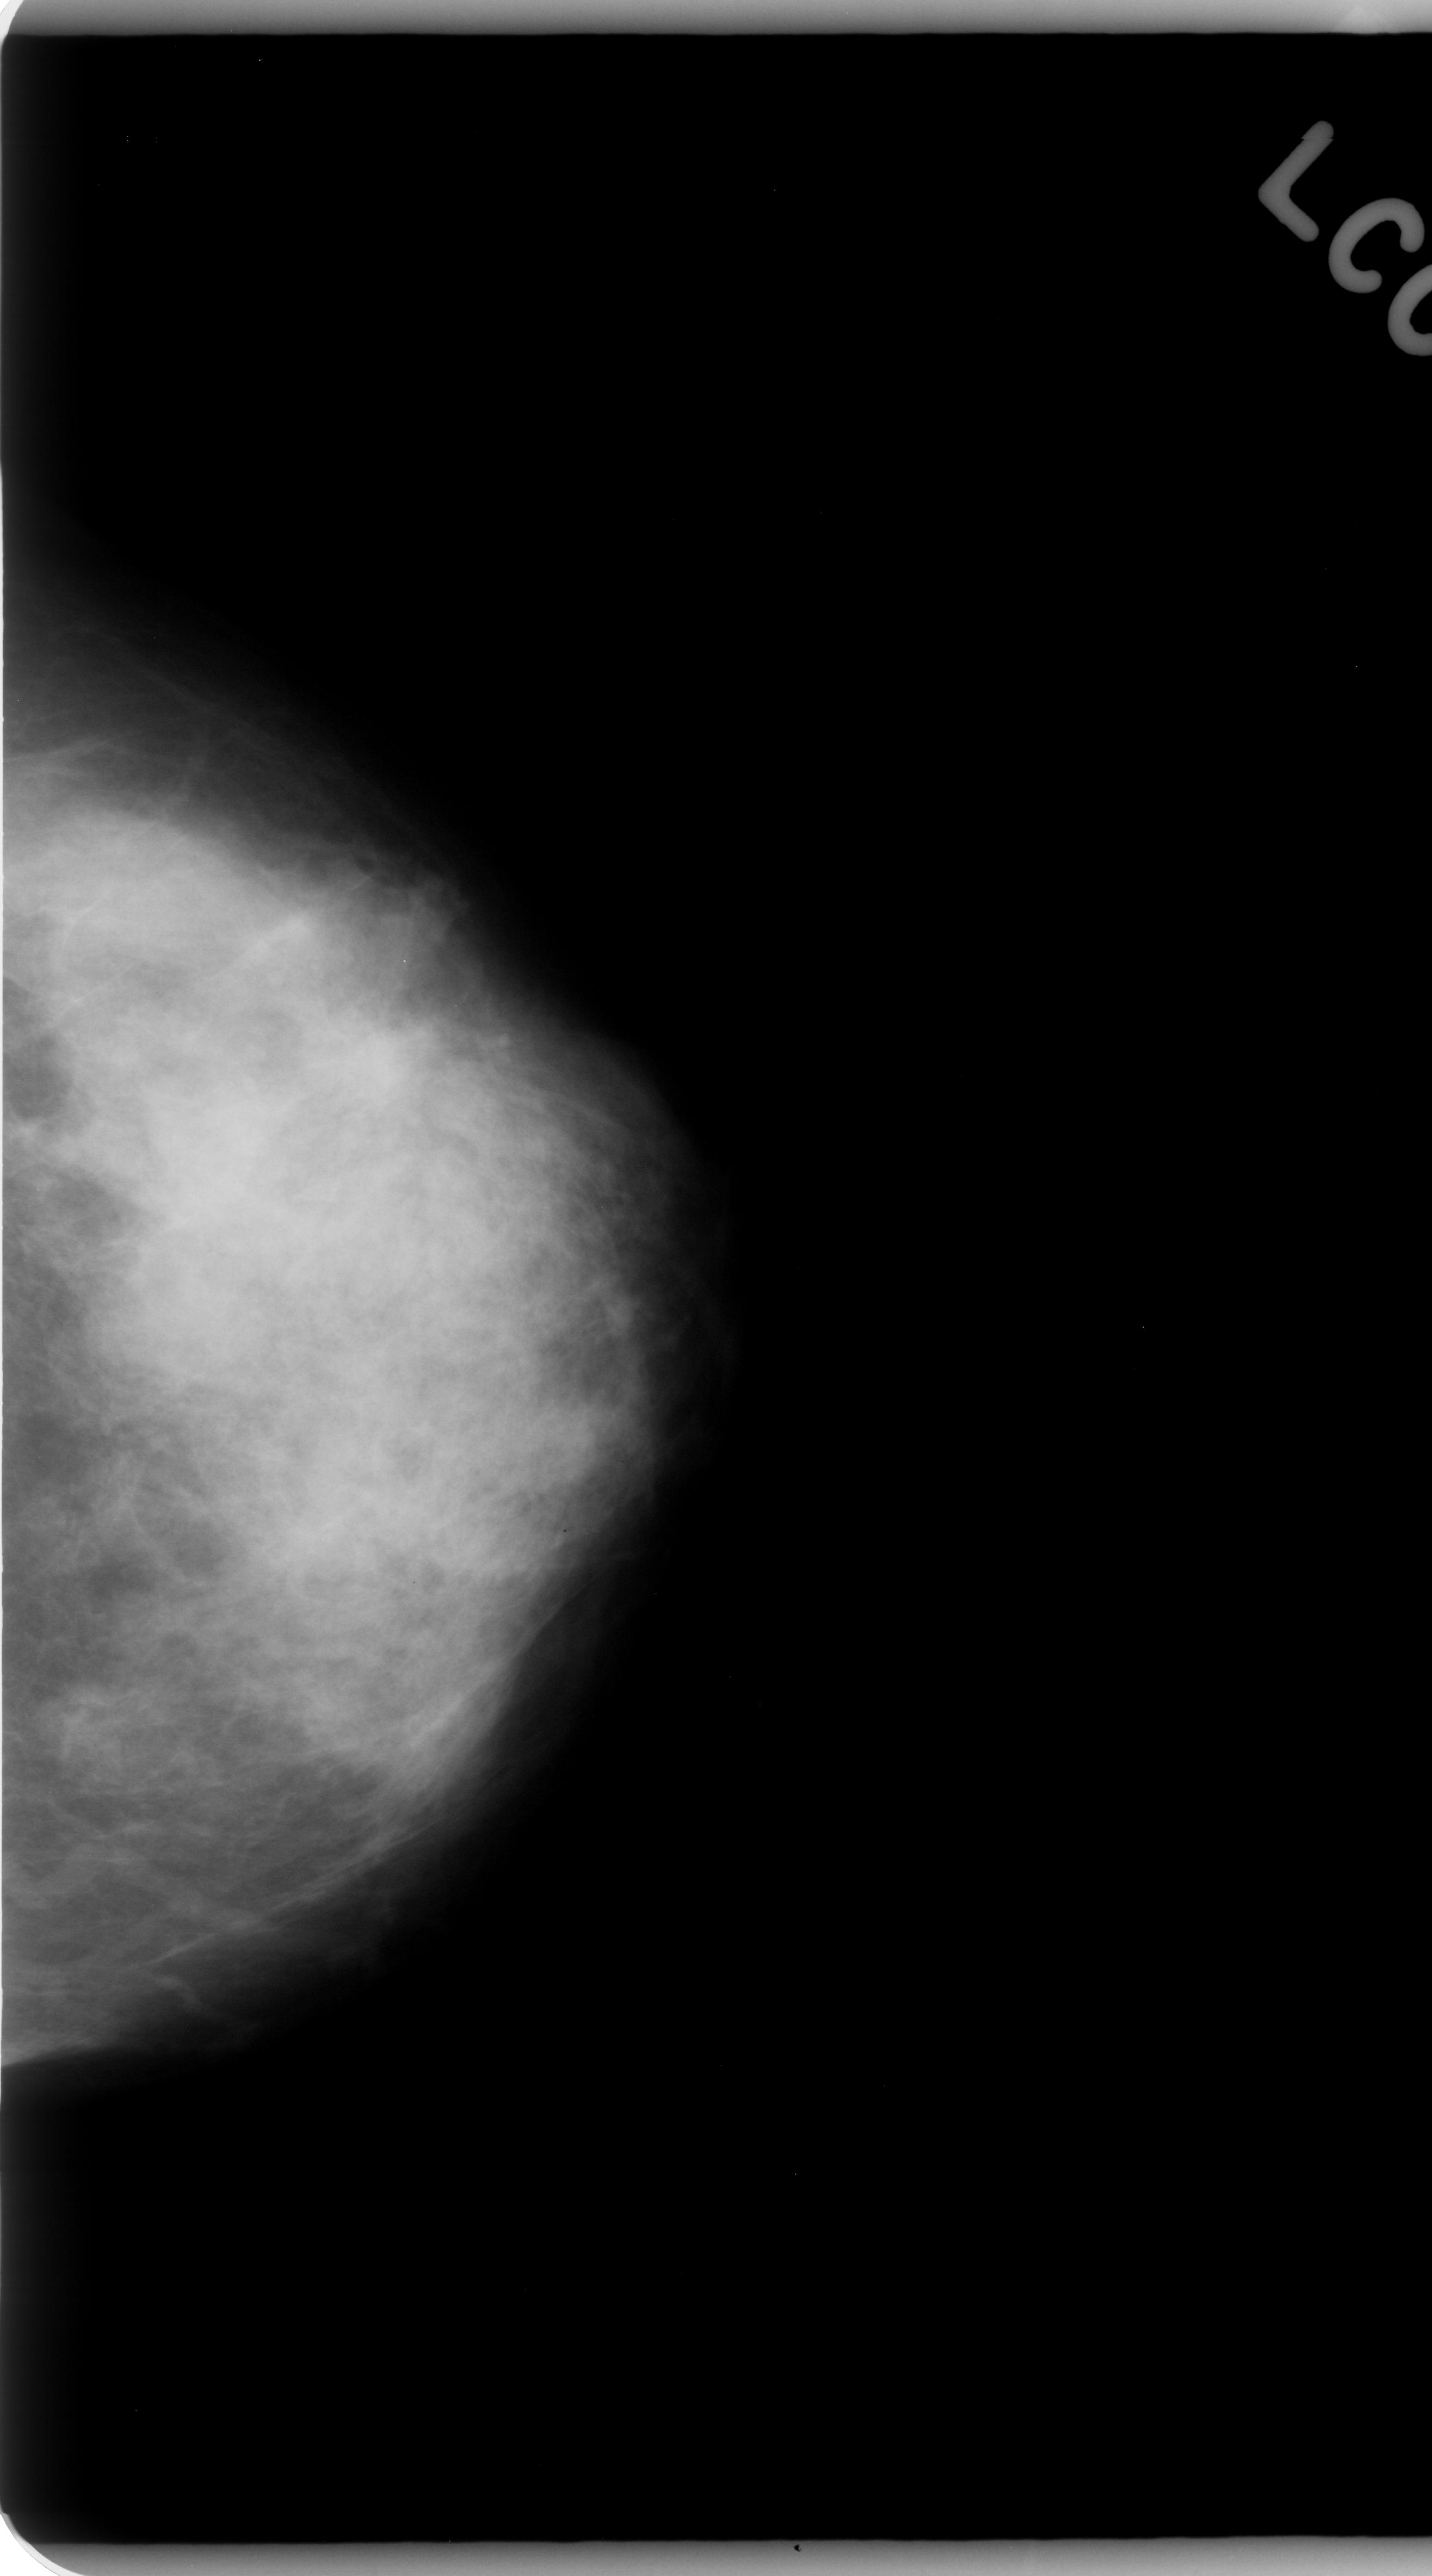
Mammogram (digitized film), left breast, craniocaudal (CC) view, BI-RADS breast density category 4 (scale 1–4).
Radiologist-marked abnormalities on this image: mass, shape irregular, margins spiculated; BI-RADS assessment category 5; pathology (as recorded): malignant.